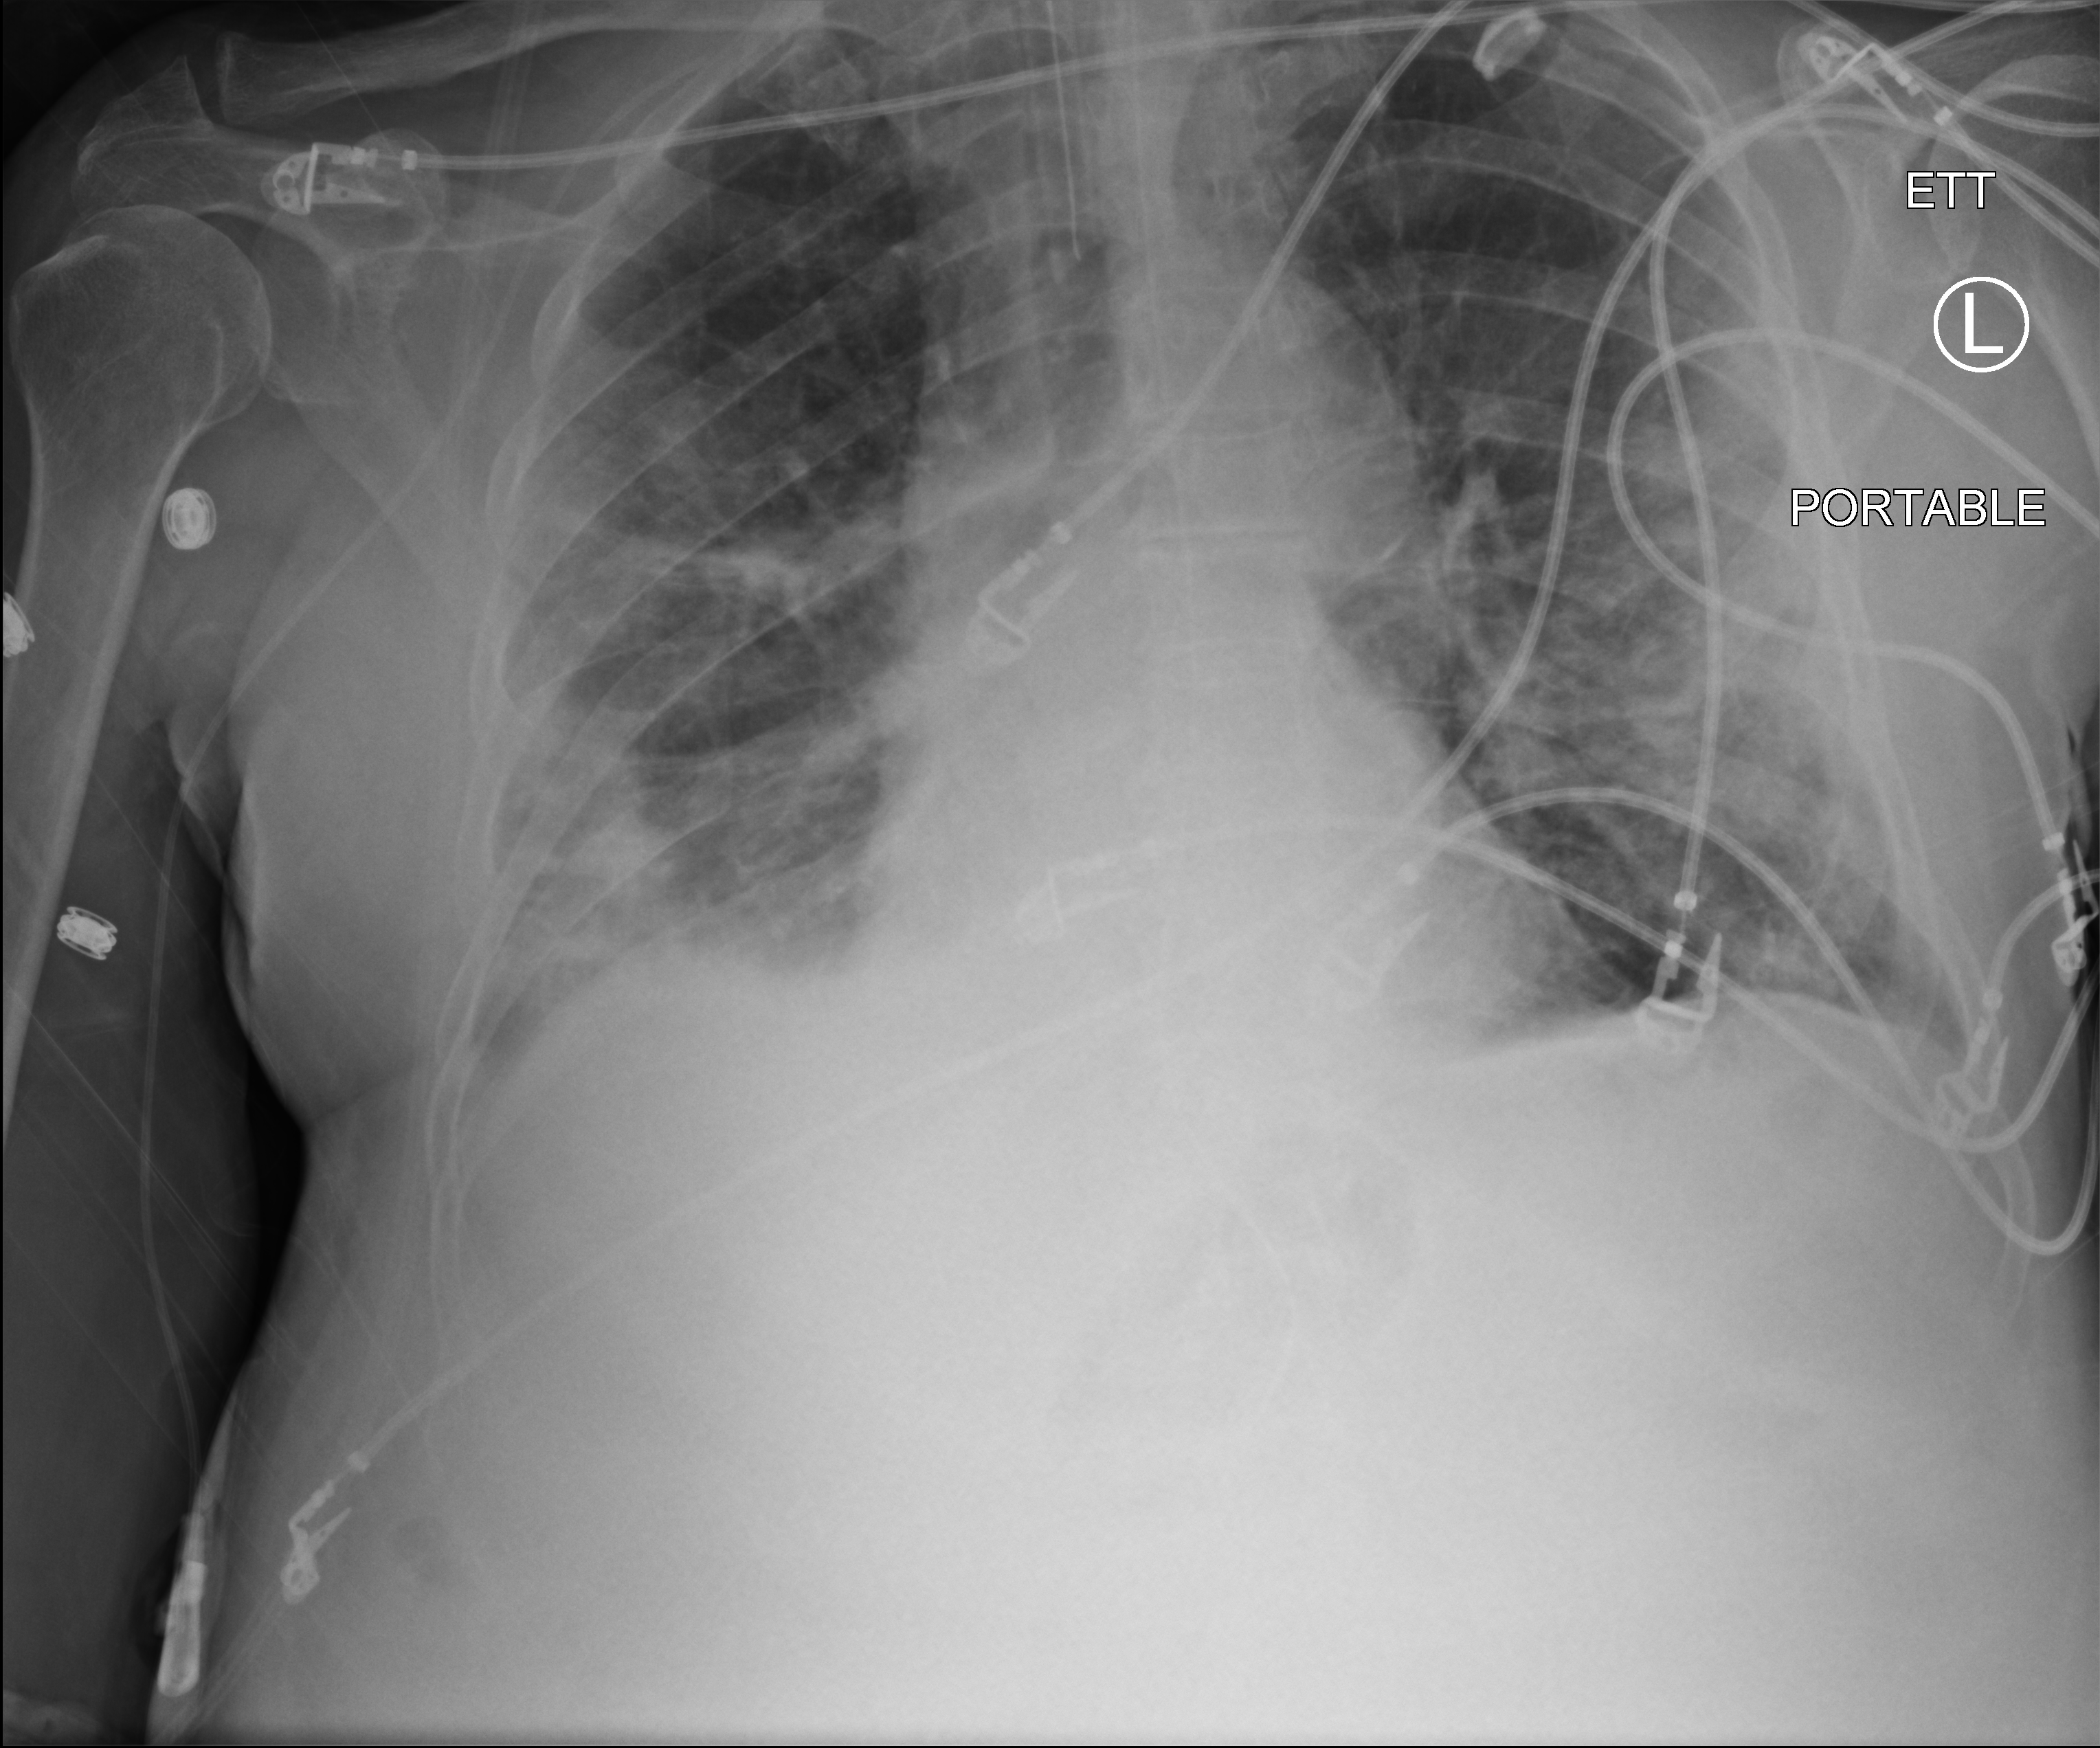
Bedside chest radiograph (computed radiography); anteroposterior (AP) projection. Patient hospitalised with COVID-19; male, aged 75–90 years.
Admission-level facts for this patient (not findings on this image; timing relative to this image not recorded):
- length of hospital stay: 70 days